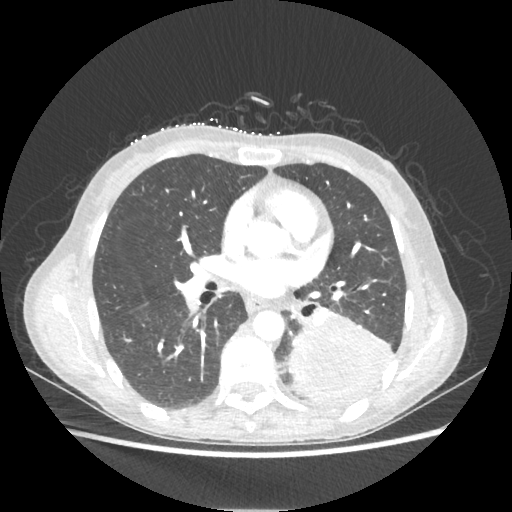
Chest CT, one axial slice. Position 112 of 221 along the scan axis. Reconstruction kernel STANDARD. Lung window (W 1500 / L -600 HU). 1.25 mm slice thickness. 512 × 512 image matrix. Female patient, age 53 years. Case-level facts recorded for this patient, not image findings: clinical TNM (as recorded): T3 N0 M0.
Structures marked on this image (bounding box drawn by a radiologist):
- lung tumour (recorded histology: adenocarcinoma): bounding box <290,311,393,401> (left, top, right, bottom; pixels)